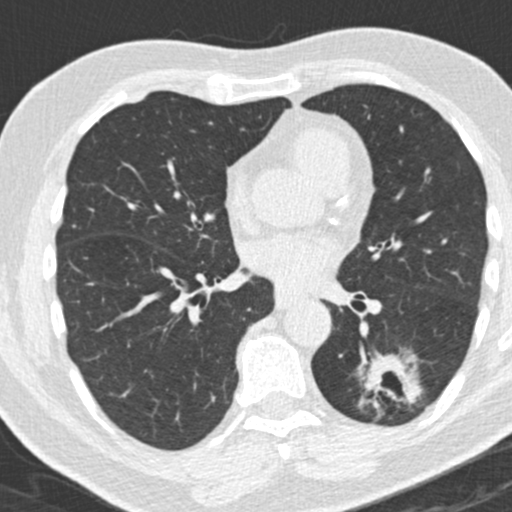
Axial slice from a low-dose chest CT screening exam; third annual screen; lung window (W 1500 / L -600 HU); 2 mm slice thickness; standard (soft-tissue) reconstruction kernel (B30f); 120 kVp. Male, age 66 years at enrolment. Former smoker at enrolment.
• Expert reader's lesion annotation, bounding box (x1, y1, x2, y2) in pixels: (356, 350, 426, 427).
• Screening reader's record for this exam (one nodule recorded; not confirmed to be the boxed lesion): non-calcified nodule or mass ≥4 mm, left lower lobe, 31 × 24 mm, spiculated (stellate) margins, pre-existing on the prior screen: yes; interval growth: yes.
• Lung cancer was diagnosed 56 days after this screen: adenocarcinoma, NOS, left lower lobe, poorly differentiated (G3), stage IB (AJCC 6th edition), 38 mm at pathology.